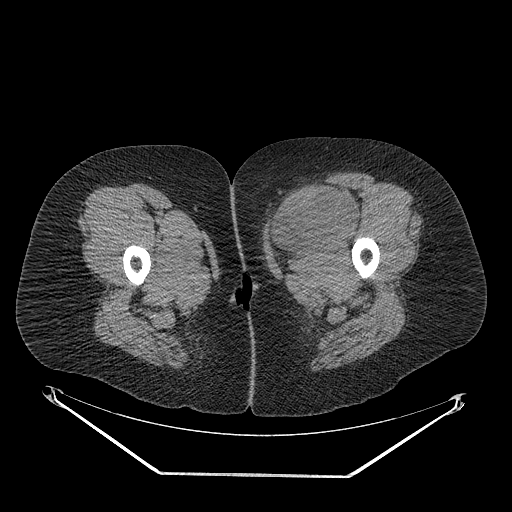
CT of an extremity soft-tissue mass (from a PET/CT study), one axial slice; reconstruction kernel STANDARD; 140 kVp; soft-tissue window (W 400 / L 40 HU); 512 × 512 image matrix, field of view 500 × 500 mm. Female patient. Case-level facts recorded for this patient, not image findings: histological type: myxofibrosarcoma; grade: intermediate; site of the primary tumour: left thigh.
Outlined on this slice (expert contour drawn on MRI and transferred to this co-registered scan by the dataset authors):
- gross tumour volume including surrounding oedema: bounding box (x1, y1, x2, y2) in pixels: (267, 187, 359, 263)
- gross tumour volume (mass): (267, 187, 355, 248)